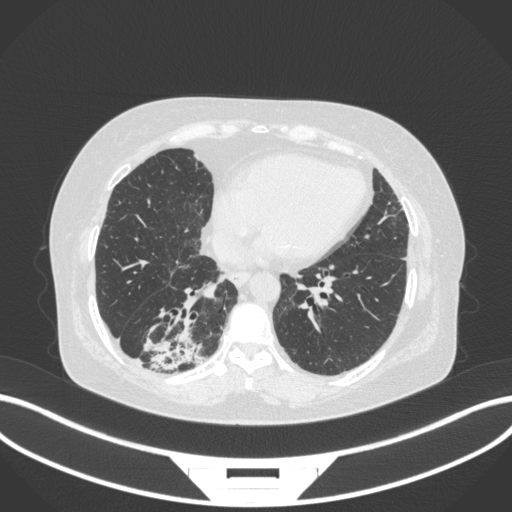
Chest CT, one axial slice. Slice 77 of 303 in the series (ordered by position). 120 kVp. Lung window (W 1500 / L -600 HU). 512 × 512 image matrix. Female patient, age 65 years. From the clinical record (not read from this slice): clinical TNM (as recorded): T2b N1 M0; histopathological grade: G1.
Outlined on this slice (rectangle marked by the reading radiologist):
- lung tumour (recorded histology: adenocarcinoma): box from (x=140, y=308) to (x=203, y=372) px